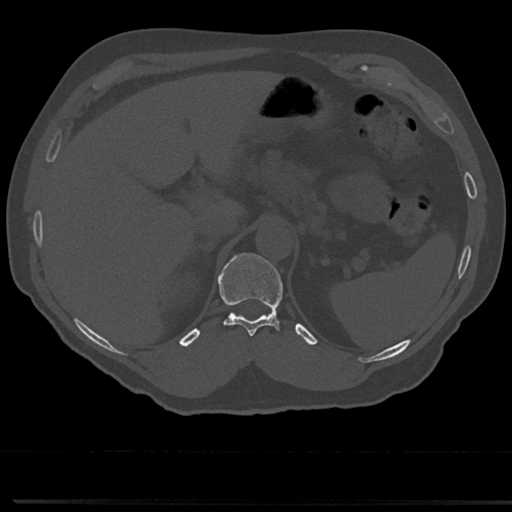
CT including the spine, one axial slice; 120 kVp; bone window (W 1800 / L 400 HU); 0.5 mm slice thickness; 512 × 512 image matrix, field of view 355 × 355 mm. Male patient, age 61 years. From the clinical record (not read from this slice): primary cancer: prostate.
Structures marked on this image (semi-automatic segmentation, software-assisted and operator-edited):
- T11 vertebra: box from (x=218, y=253) to (x=283, y=338) px